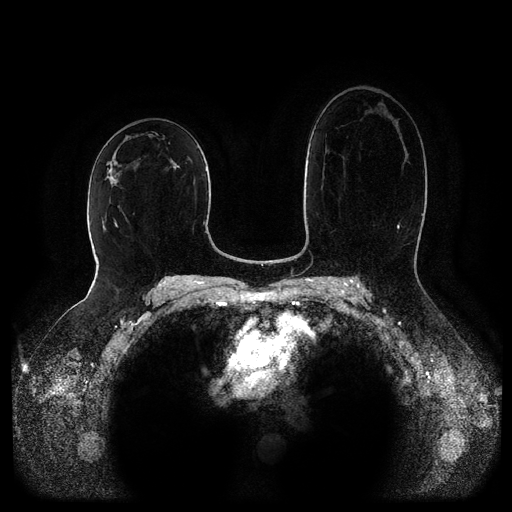
Breast MRI (dynamic contrast-enhanced, multi-phase), one axial slice; slice 56 of 116 in the series (ordered by position); dynamic contrast-enhanced series, time point 2 of 5 at this slice position (early post-contrast); 1.5 T; TE 2.6 ms, TR 5.2 ms; 2 mm slice thickness; 512 × 512 image matrix, field of view 380 × 380 mm. Female patient, age 52 years.
Annotated regions visible in this slice (semi-automatic segmentation, software-assisted and operator-edited):
- breast lesion (labelled 'tumour' in the annotation; benign lesions carry a separate 'benign' label): box from (x=166, y=159) to (x=180, y=170) px